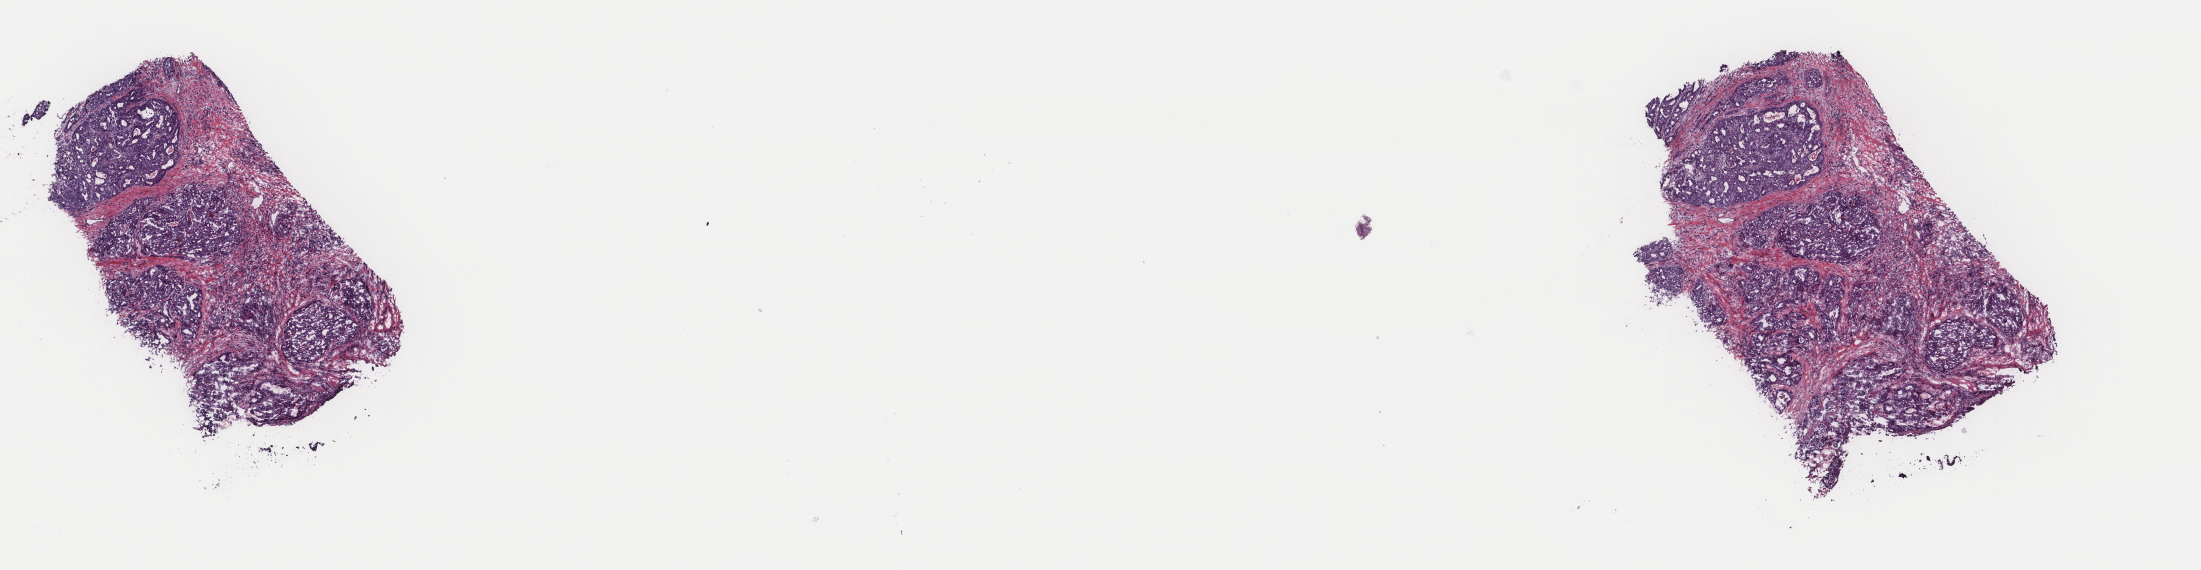
H&E whole-slide image — a low-resolution overview of the entire scanned area, about 17.5 x 4.5 mm (acquisition: 40x scan), frozen section from the top of the tissue portion, primary tumour sample from the stomach. Male, age 68 years at initial diagnosis. Histologic grade: G2 (moderately differentiated). Composition of this section per pathologist review: tumour cells 100%, tumour nuclei 75%, normal cells 0%, stromal cells 0%, necrosis 0%. Inflammatory infiltration, as recorded: lymphocyte infiltration 3%, monocyte infiltration 0%, neutrophil infiltration 0%.
TNM: T3 N0 M0. Pathologic diagnosis: Adenocarcinoma, NOS. AJCC pathologic stage: IIA (7th edition).